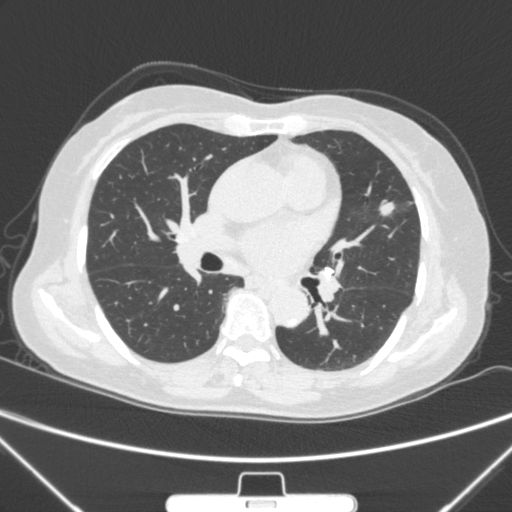
Chest CT, one axial slice; slice 149 of 300 in the series (ordered by position); 120 kVp; lung window (W 1500 / L -600 HU); 1 mm slice thickness; 512 × 512 image matrix, field of view 350 × 350 mm. Female patient, age 70 years. From the clinical record (not read from this slice): clinical TNM (as recorded): T1b N0 M0; histopathological grade: G2.
Annotated regions visible in this slice (bounding box drawn by a radiologist):
- lung tumour (recorded histology: adenocarcinoma): bounding box (x1, y1, x2, y2) in pixels: (373, 193, 396, 225)